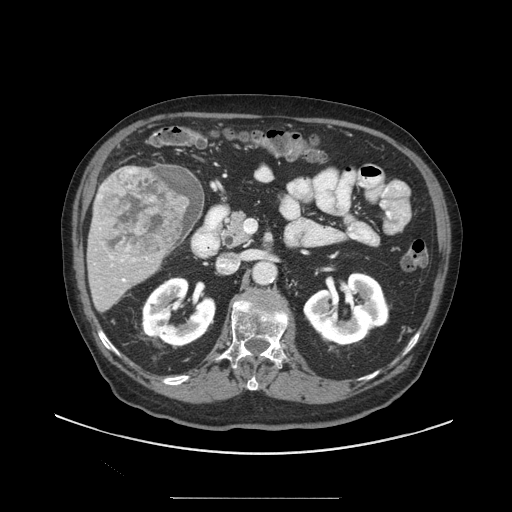
Contrast-enhanced abdominal CT (liver protocol), one axial slice; position 44 of 97 along the scan axis; soft-tissue window (W 400 / L 40 HU); 2.5 mm slice thickness; 512 × 512 image matrix. Case-level facts recorded for this patient, not image findings: diagnosis: hepatocellular carcinoma (patient treated with transarterial chemoembolisation; whether this scan precedes or follows treatment is not stated here); TNM stage (as recorded): Stage-IIIC; Child-Pugh class: A; tumour size: 9.2 cm.
Outlined on this slice (semi-automatic segmentation, software-assisted and operator-edited):
- liver parenchyma outside the tumour (the mass and vessels are separate outlines, so this box may not span the whole liver): bounding box <86,164,202,312> (left, top, right, bottom; pixels)
- mass: <94,165,189,259>
- liver vessels: <110,256,126,282>